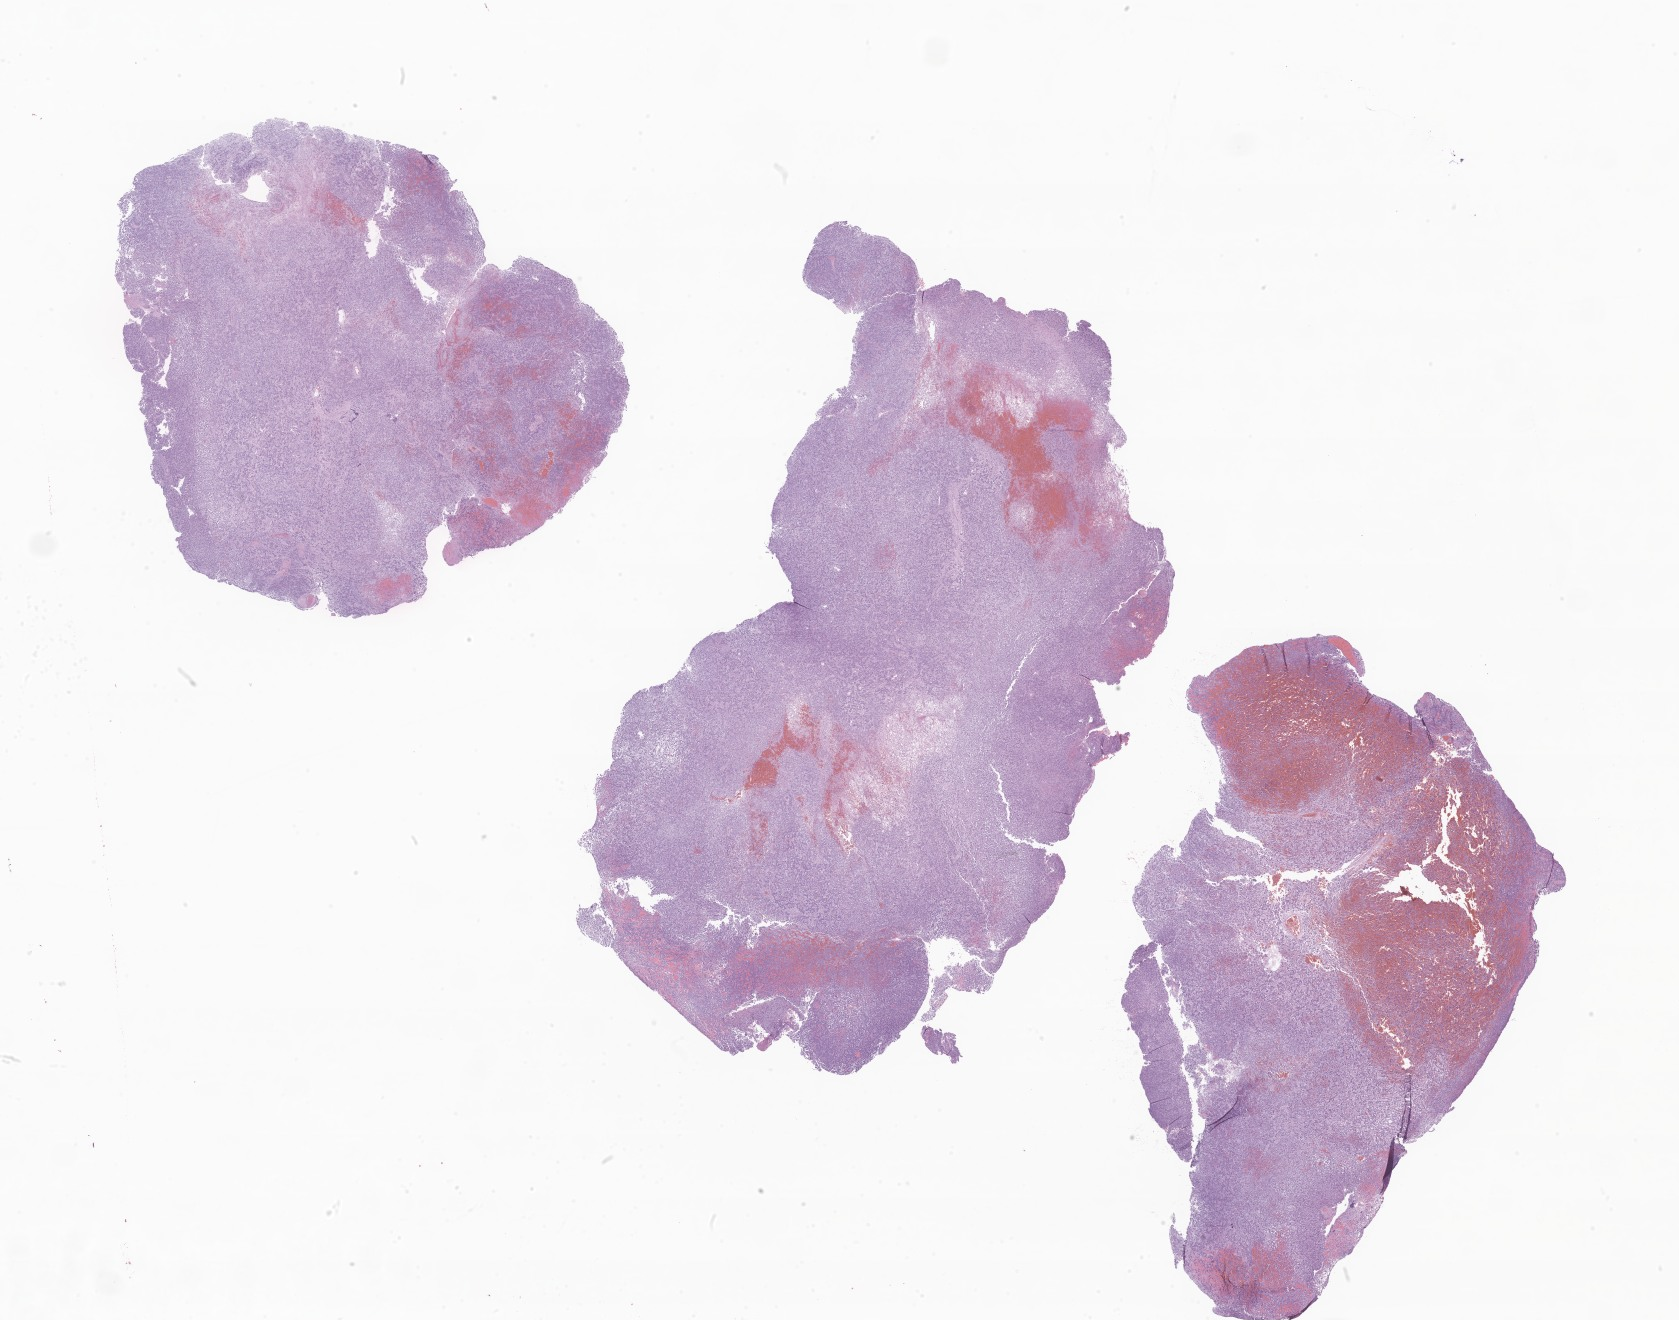
H&E whole-slide image of tumor tissue from the brain — whole scanned area (about 28.3 x 22.3 mm) shown as a low-resolution overview. FFPE section. Patient: female, age 110 months (9 years 2 months).
Recorded diagnosis: Neoplasm, uncertain whether benign or malignant.